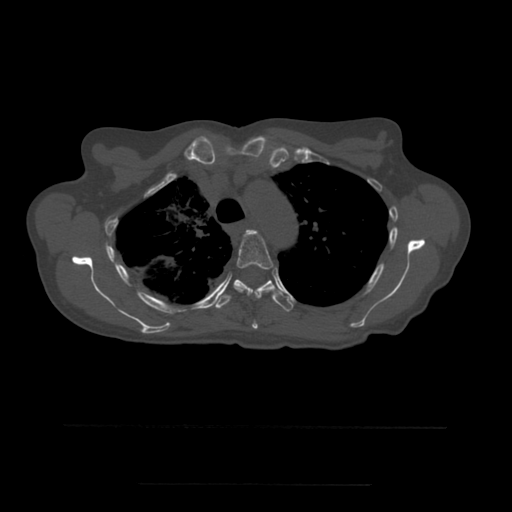
CT including the spine, one axial slice; position 402 of 544 along the scan axis; bone window (W 1800 / L 400 HU); 512 × 512 image matrix. Patient age 58 years. Case-level facts recorded for this patient, not image findings: primary cancer: lung.
Outlined on this slice (semi-automatic segmentation, software-assisted and operator-edited):
- T4 vertebra: bounding box <234,230,274,329> (left, top, right, bottom; pixels)
- T5 vertebra: <216,279,294,311>